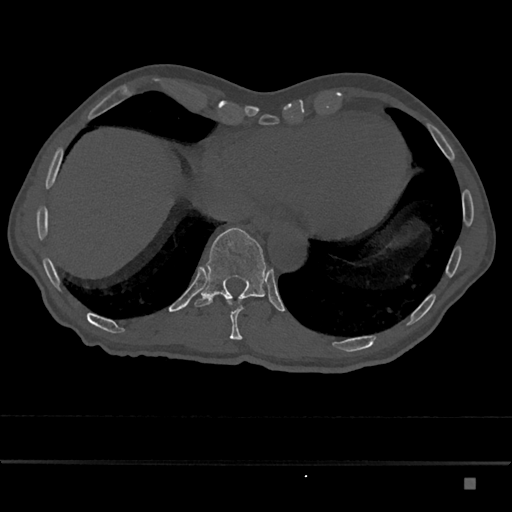
CT including the spine, one axial slice; position 704 of 797 along the scan axis; reconstruction kernel Br40s/3; 120 kVp; bone window (W 1800 / L 400 HU); 0.5 mm slice thickness; 512 × 512 image matrix. Male patient, age 72 years. From the clinical record (not read from this slice): primary cancer: prostate.
Structures marked on this image (semi-automatic segmentation, software-assisted and operator-edited):
- T10 vertebra: bounding box [x1, y1, x2, y2] px = [226, 298, 243, 340]
- T11 vertebra: [194, 227, 267, 307]